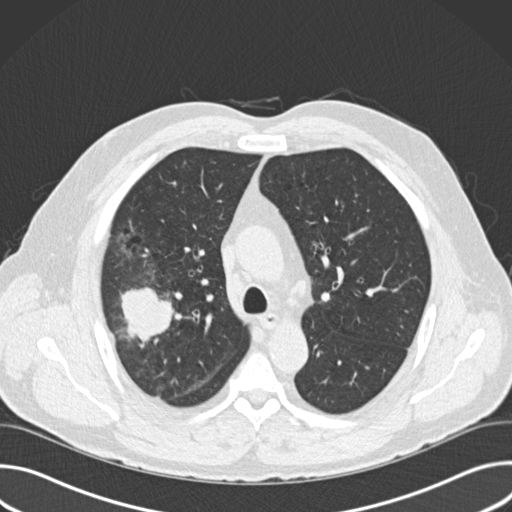
Low-dose screening chest CT, one axial slice. Slice 111 of 157 in the series (ordered by position). Reconstruction kernel B30f. 120 kVp. Lung window (W 1500 / L -600 HU). 512 × 512 image matrix, field of view 380 × 380 mm.
Structures marked on this image (manually delineated by an expert):
- lesion 1 (tumor, upper lobe of right lung): bounding box [x1, y1, x2, y2] px = [121, 287, 174, 343]